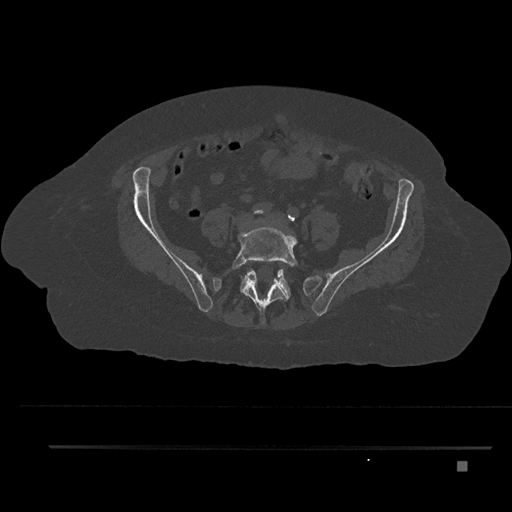
CT including the spine, one axial slice; position 36 of 797 along the scan axis; reconstruction kernel Br40s/3; 120 kVp; bone window (W 1800 / L 400 HU); 0.5 mm slice thickness; 512 × 512 image matrix, field of view 437 × 437 mm. Female patient, age 76 years. Case-level facts recorded for this patient, not image findings: primary cancer: lung; vertebrae with lytic lesions (as recorded): T11, L3.
Structures marked on this image (semi-automatically segmented with operator editing):
- L5 vertebra: box from (x=232, y=227) to (x=298, y=324) px